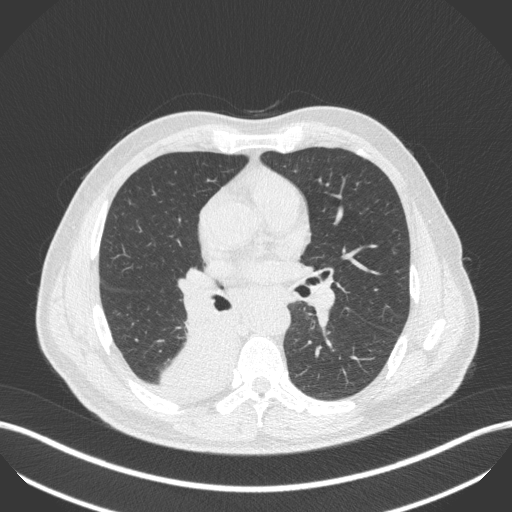
Chest CT, one axial slice; slice 257 of 451 in the series (ordered by position); 100 kVp; lung window (W 1500 / L -600 HU); 1 mm slice thickness; 512 × 512 image matrix. Male patient, age 61 years. From the clinical record (not read from this slice): clinical TNM (as recorded): T1 N0 M0.
Annotated regions visible in this slice (bounding box drawn by a radiologist):
- lung tumour (recorded histology: small cell carcinoma): bounding box <162,327,241,402> (left, top, right, bottom; pixels)